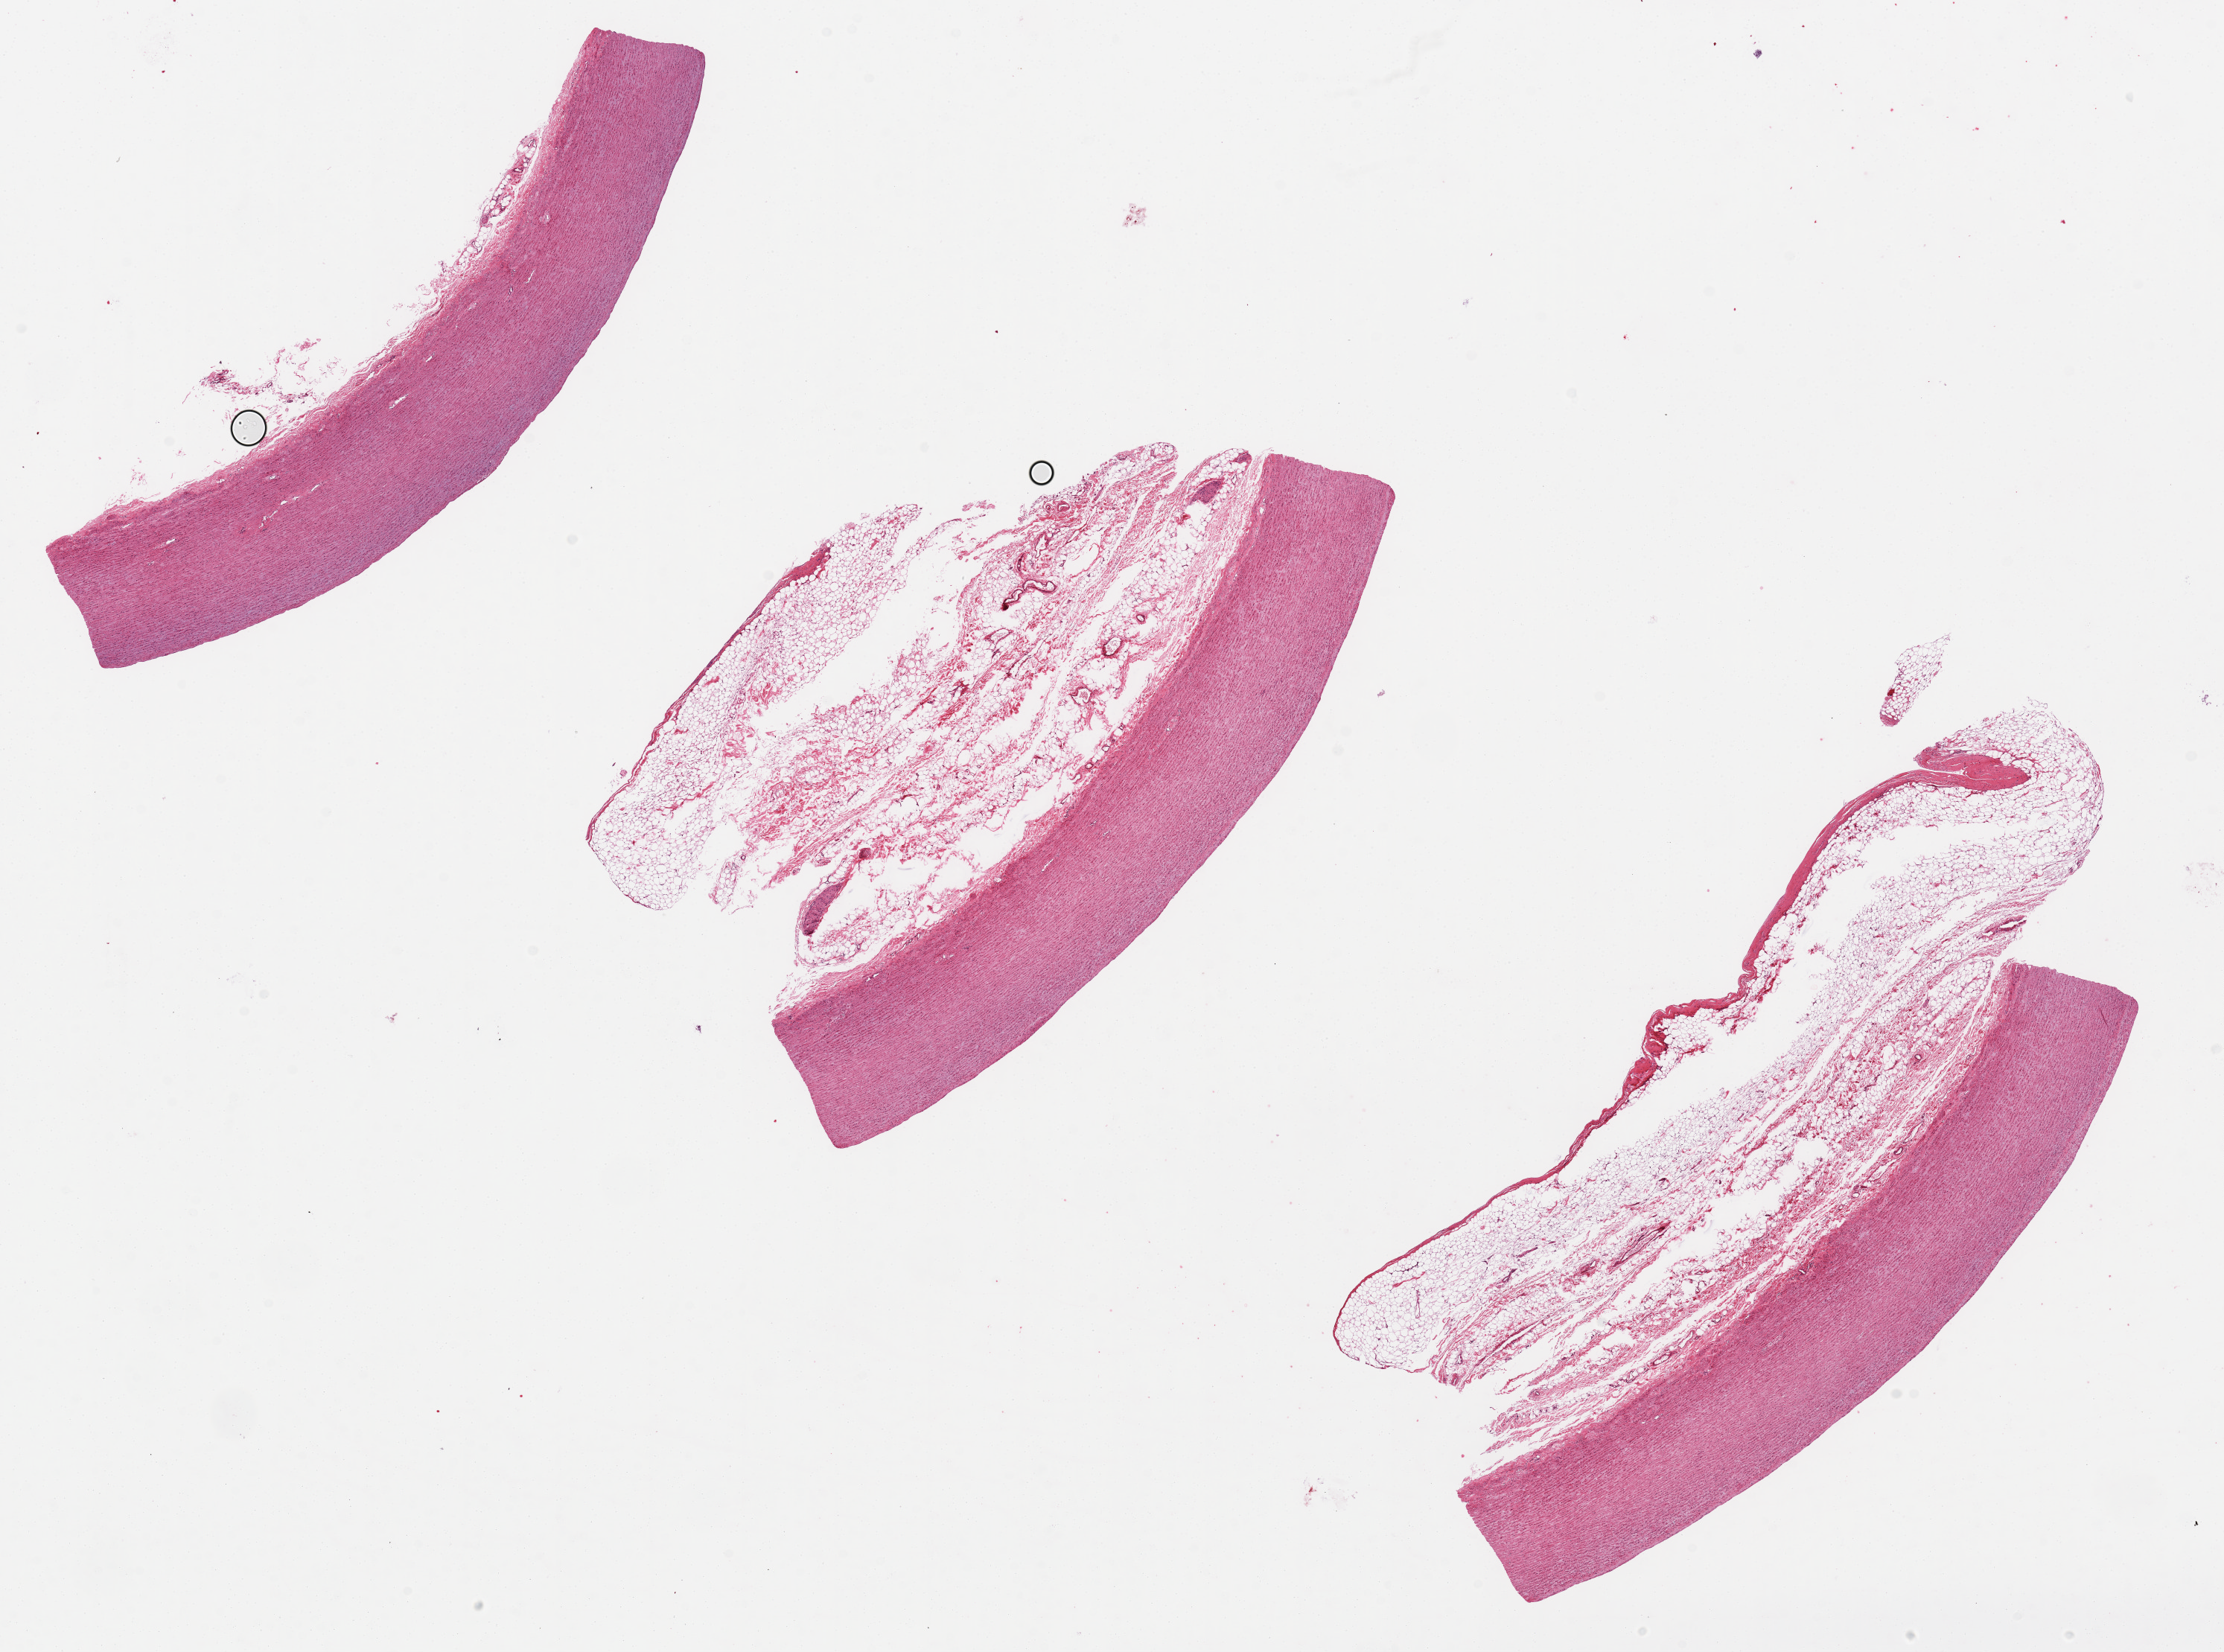
H&E whole-slide image, brightfield — low-resolution overview of the scanned area, about 23.6 x 17.6 mm (from a 20x scan), PAXgene-fixed, paraffin-embedded tissue, sampled site (target tissue): aorta, tissue donor sample. Donor sex: male.
Reviewer comment on this tissue sample: Perimural fat =50% aliquot. 8.5mm long; wall 1.5; fat>1.5mm.